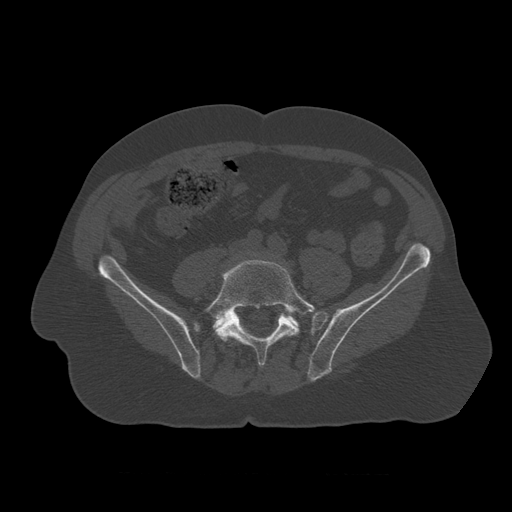
CT including the spine, one axial slice. Slice 255 of 450 in the series (ordered by position). Reconstruction kernel STANDARD. Bone window (W 1800 / L 400 HU). 1.25 mm slice thickness. 512 × 512 image matrix, field of view 405 × 405 mm. Patient age 75 years. Case-level facts recorded for this patient, not image findings: primary cancer: prostate.
Outlined on this slice (semi-automatically segmented with operator editing):
- L4 vertebra: bounding box <253,252,256,256> (left, top, right, bottom; pixels)
- L5 vertebra: <205,260,318,368>